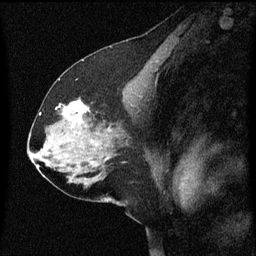
Breast MRI (dynamic contrast-enhanced), one sagittal slice; slice 33 of 60 in the series (ordered by position); dynamic contrast-enhanced series, image 2 of 3 at this slice position (ordered by acquisition); 1.5 T; TE 4.2 ms, TR 8 ms; 2 mm slice thickness; 256 × 256 image matrix, field of view 200 × 200 mm. Patient: female, 58 years.
Annotated regions visible in this slice (semi-automatic segmentation, software-assisted and operator-edited):
- analysis volume of interest (the breast-tissue region the enhancement analysis was run in; not a lesion): bounding box (x1, y1, x2, y2) in pixels: (56, 98, 95, 137)
- tumour enhancement mask (voxels above the 70 % enhancement threshold inside the analysis volume of interest): (64, 102, 89, 123)